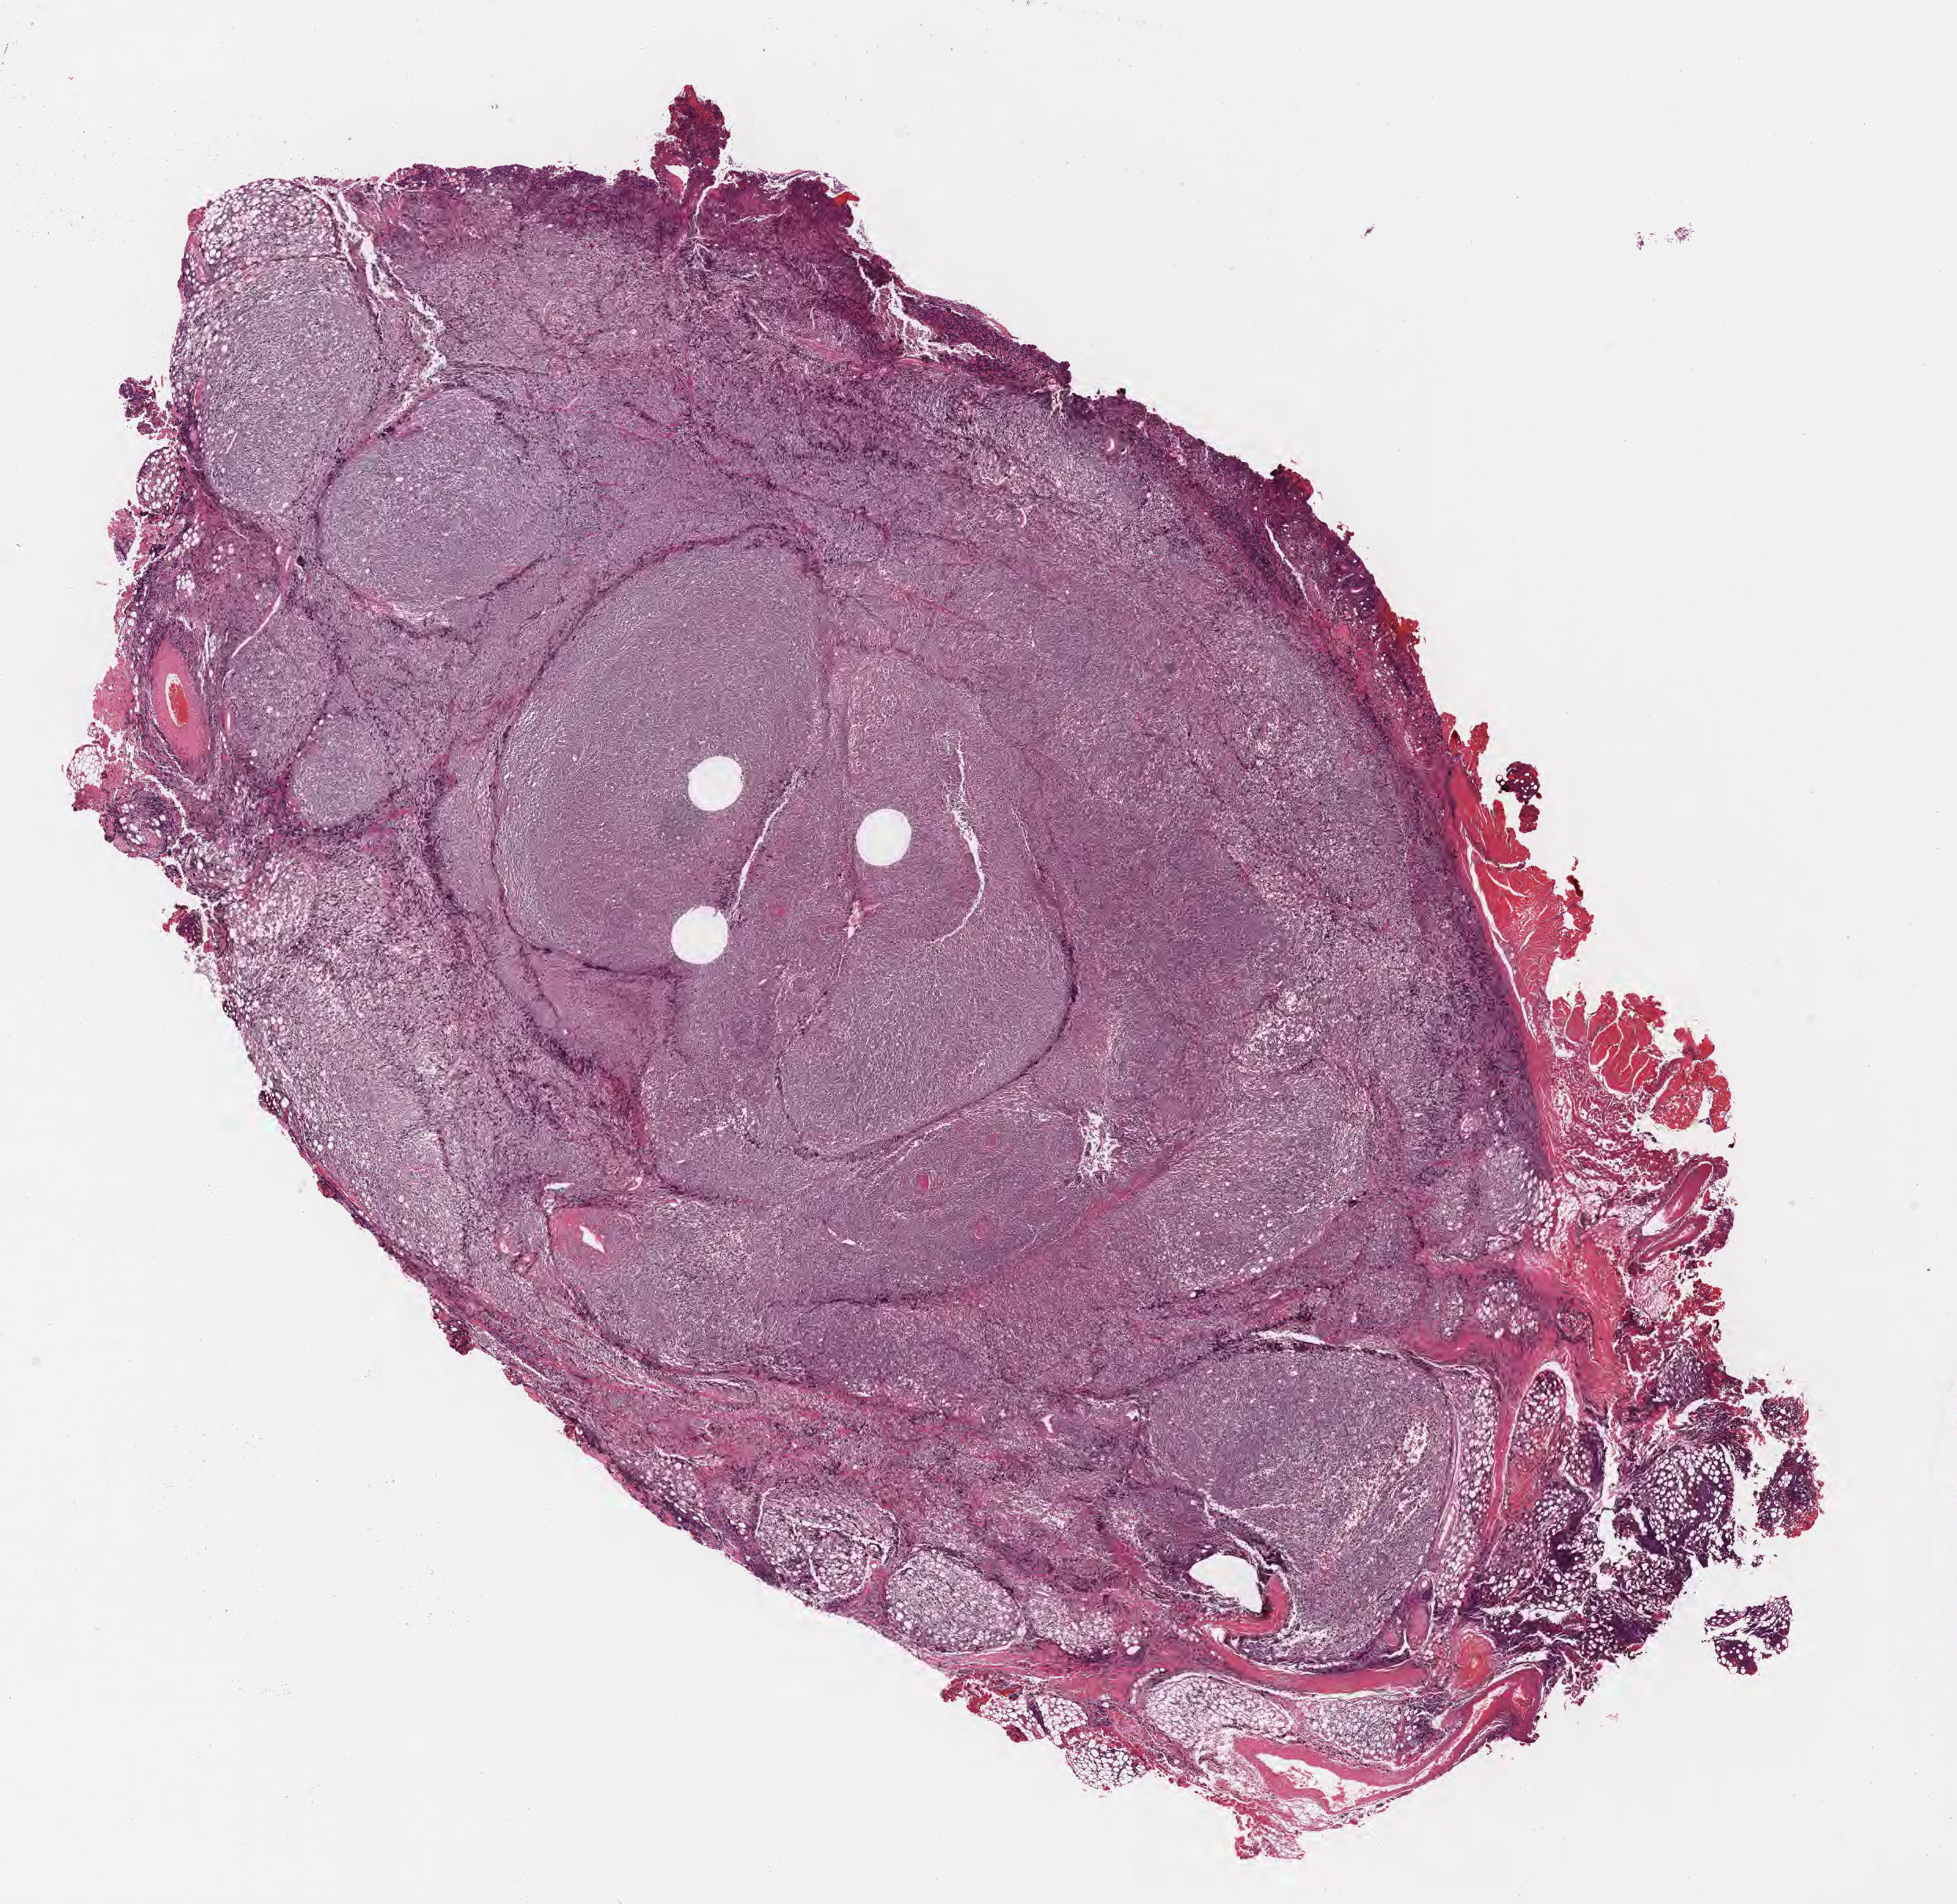
H&E whole-slide image — low-resolution overview of the scanned area, about 20.1 x 19.6 mm. FFPE section. Primary tumor. Male patient; age at initial diagnosis 4 years. Pathologist review of this section (percent, as recorded): tumor cells 85%, tumor nuclei 90%, stromal cells 10%, necrosis 0%, normal cells 5%. Infiltration values recorded for this section: lymphocyte infiltration 75%, monocyte infiltration 15%, neutrophil infiltration 0%.
Diagnosis: Burkitt lymphoma, NOS. Ann Arbor stage (patient): Stage III. Section: top of the tissue portion.